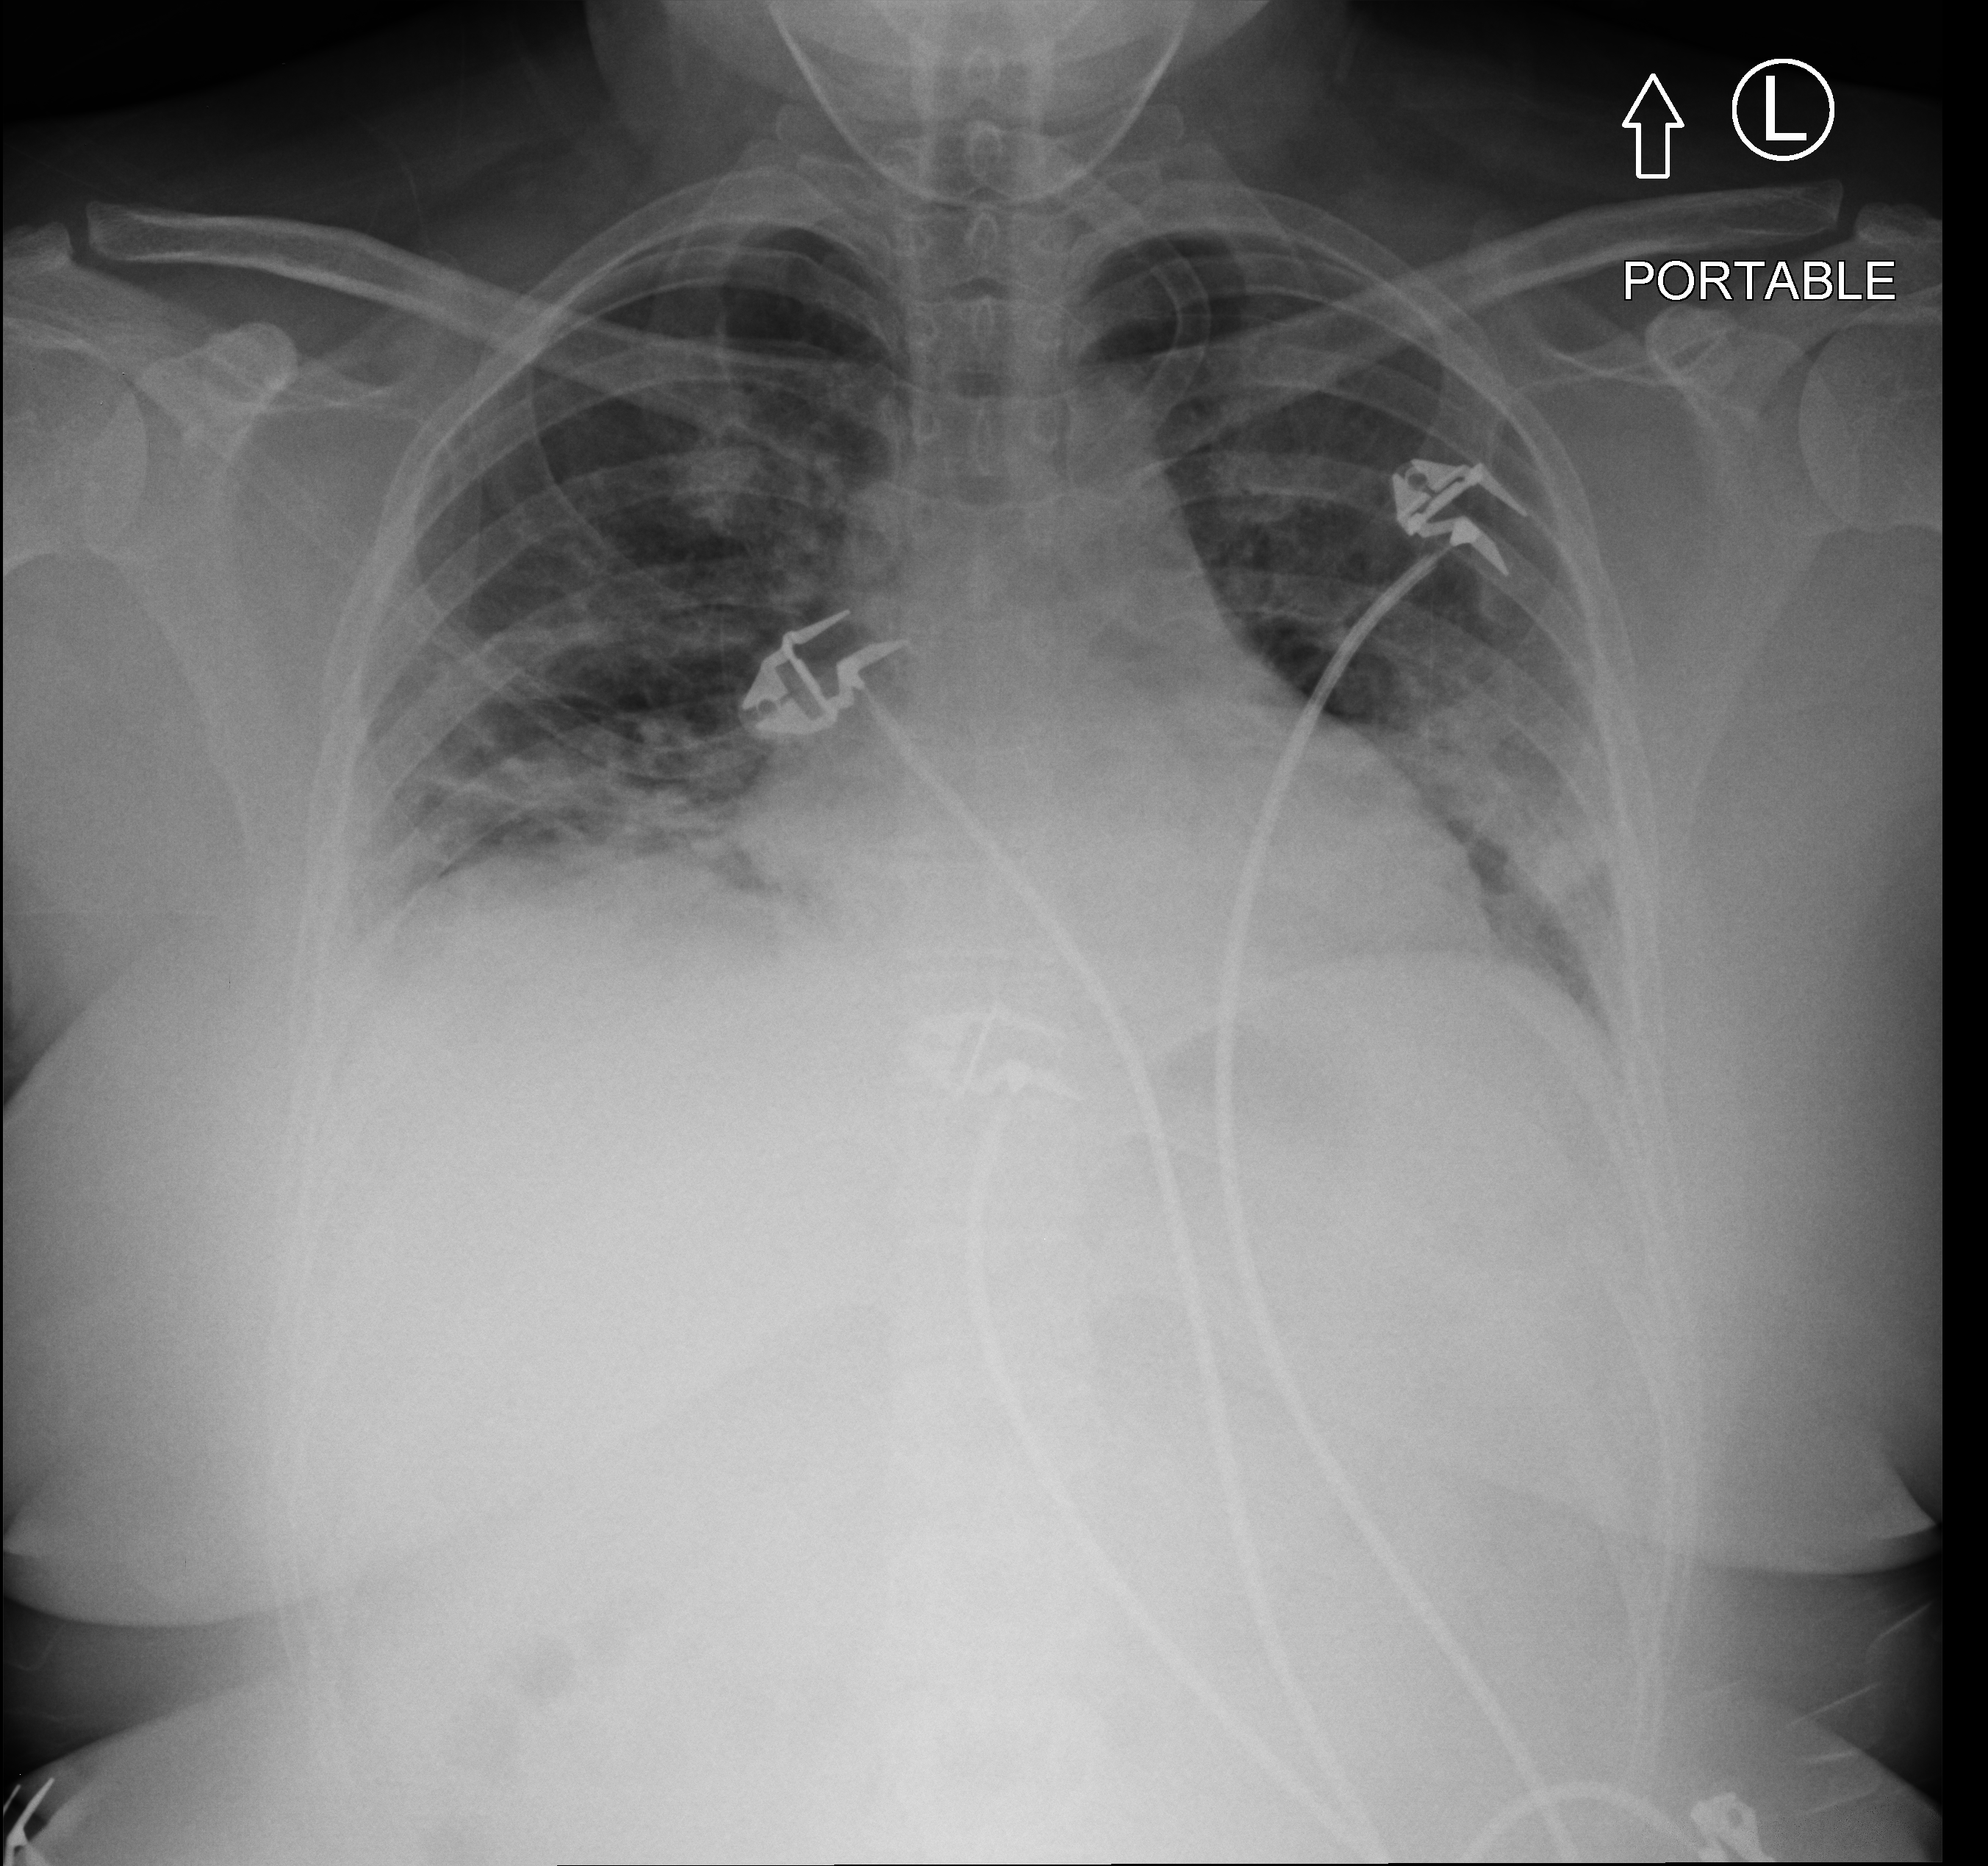
Bedside chest radiograph (computed radiography); anteroposterior (AP) projection. Patient hospitalised with COVID-19; female, aged 18–59 years.
From the hospital-stay record, not from the radiograph (when in the stay this image was taken is not recorded): length of hospital stay: 16 days; other chronic lung disease (admission record): no.